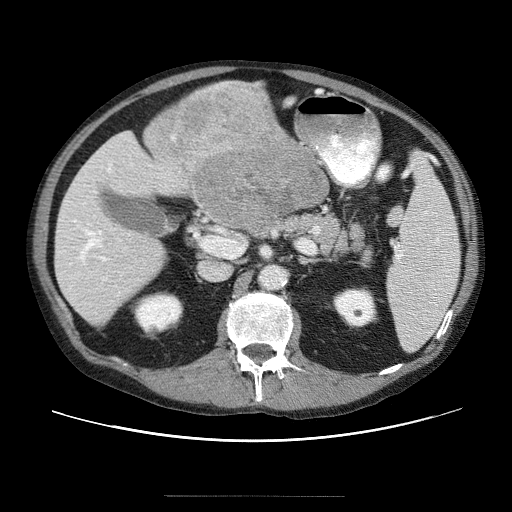
Contrast-enhanced abdominal CT (liver protocol), one axial slice. Slice 17 of 69 in the series (ordered by position). 120 kVp. Soft-tissue window (W 400 / L 40 HU). 2.5 mm slice thickness. 512 × 512 image matrix. Case-level facts recorded for this patient, not image findings: diagnosis: hepatocellular carcinoma (patient treated with transarterial chemoembolisation; whether this scan precedes or follows treatment is not stated here); TNM stage (as recorded): Stage-IVB; Child-Pugh class: B; tumour differentiation: poorly differentiated.
Outlined on this slice (semi-automatic segmentation, software-assisted and operator-edited):
- liver parenchyma outside the tumour (the mass and vessels are separate outlines, so this box may not span the whole liver): bounding box (x1, y1, x2, y2) in pixels: (54, 111, 326, 320)
- mass: (144, 83, 330, 238)
- liver vessels: (63, 155, 146, 298)